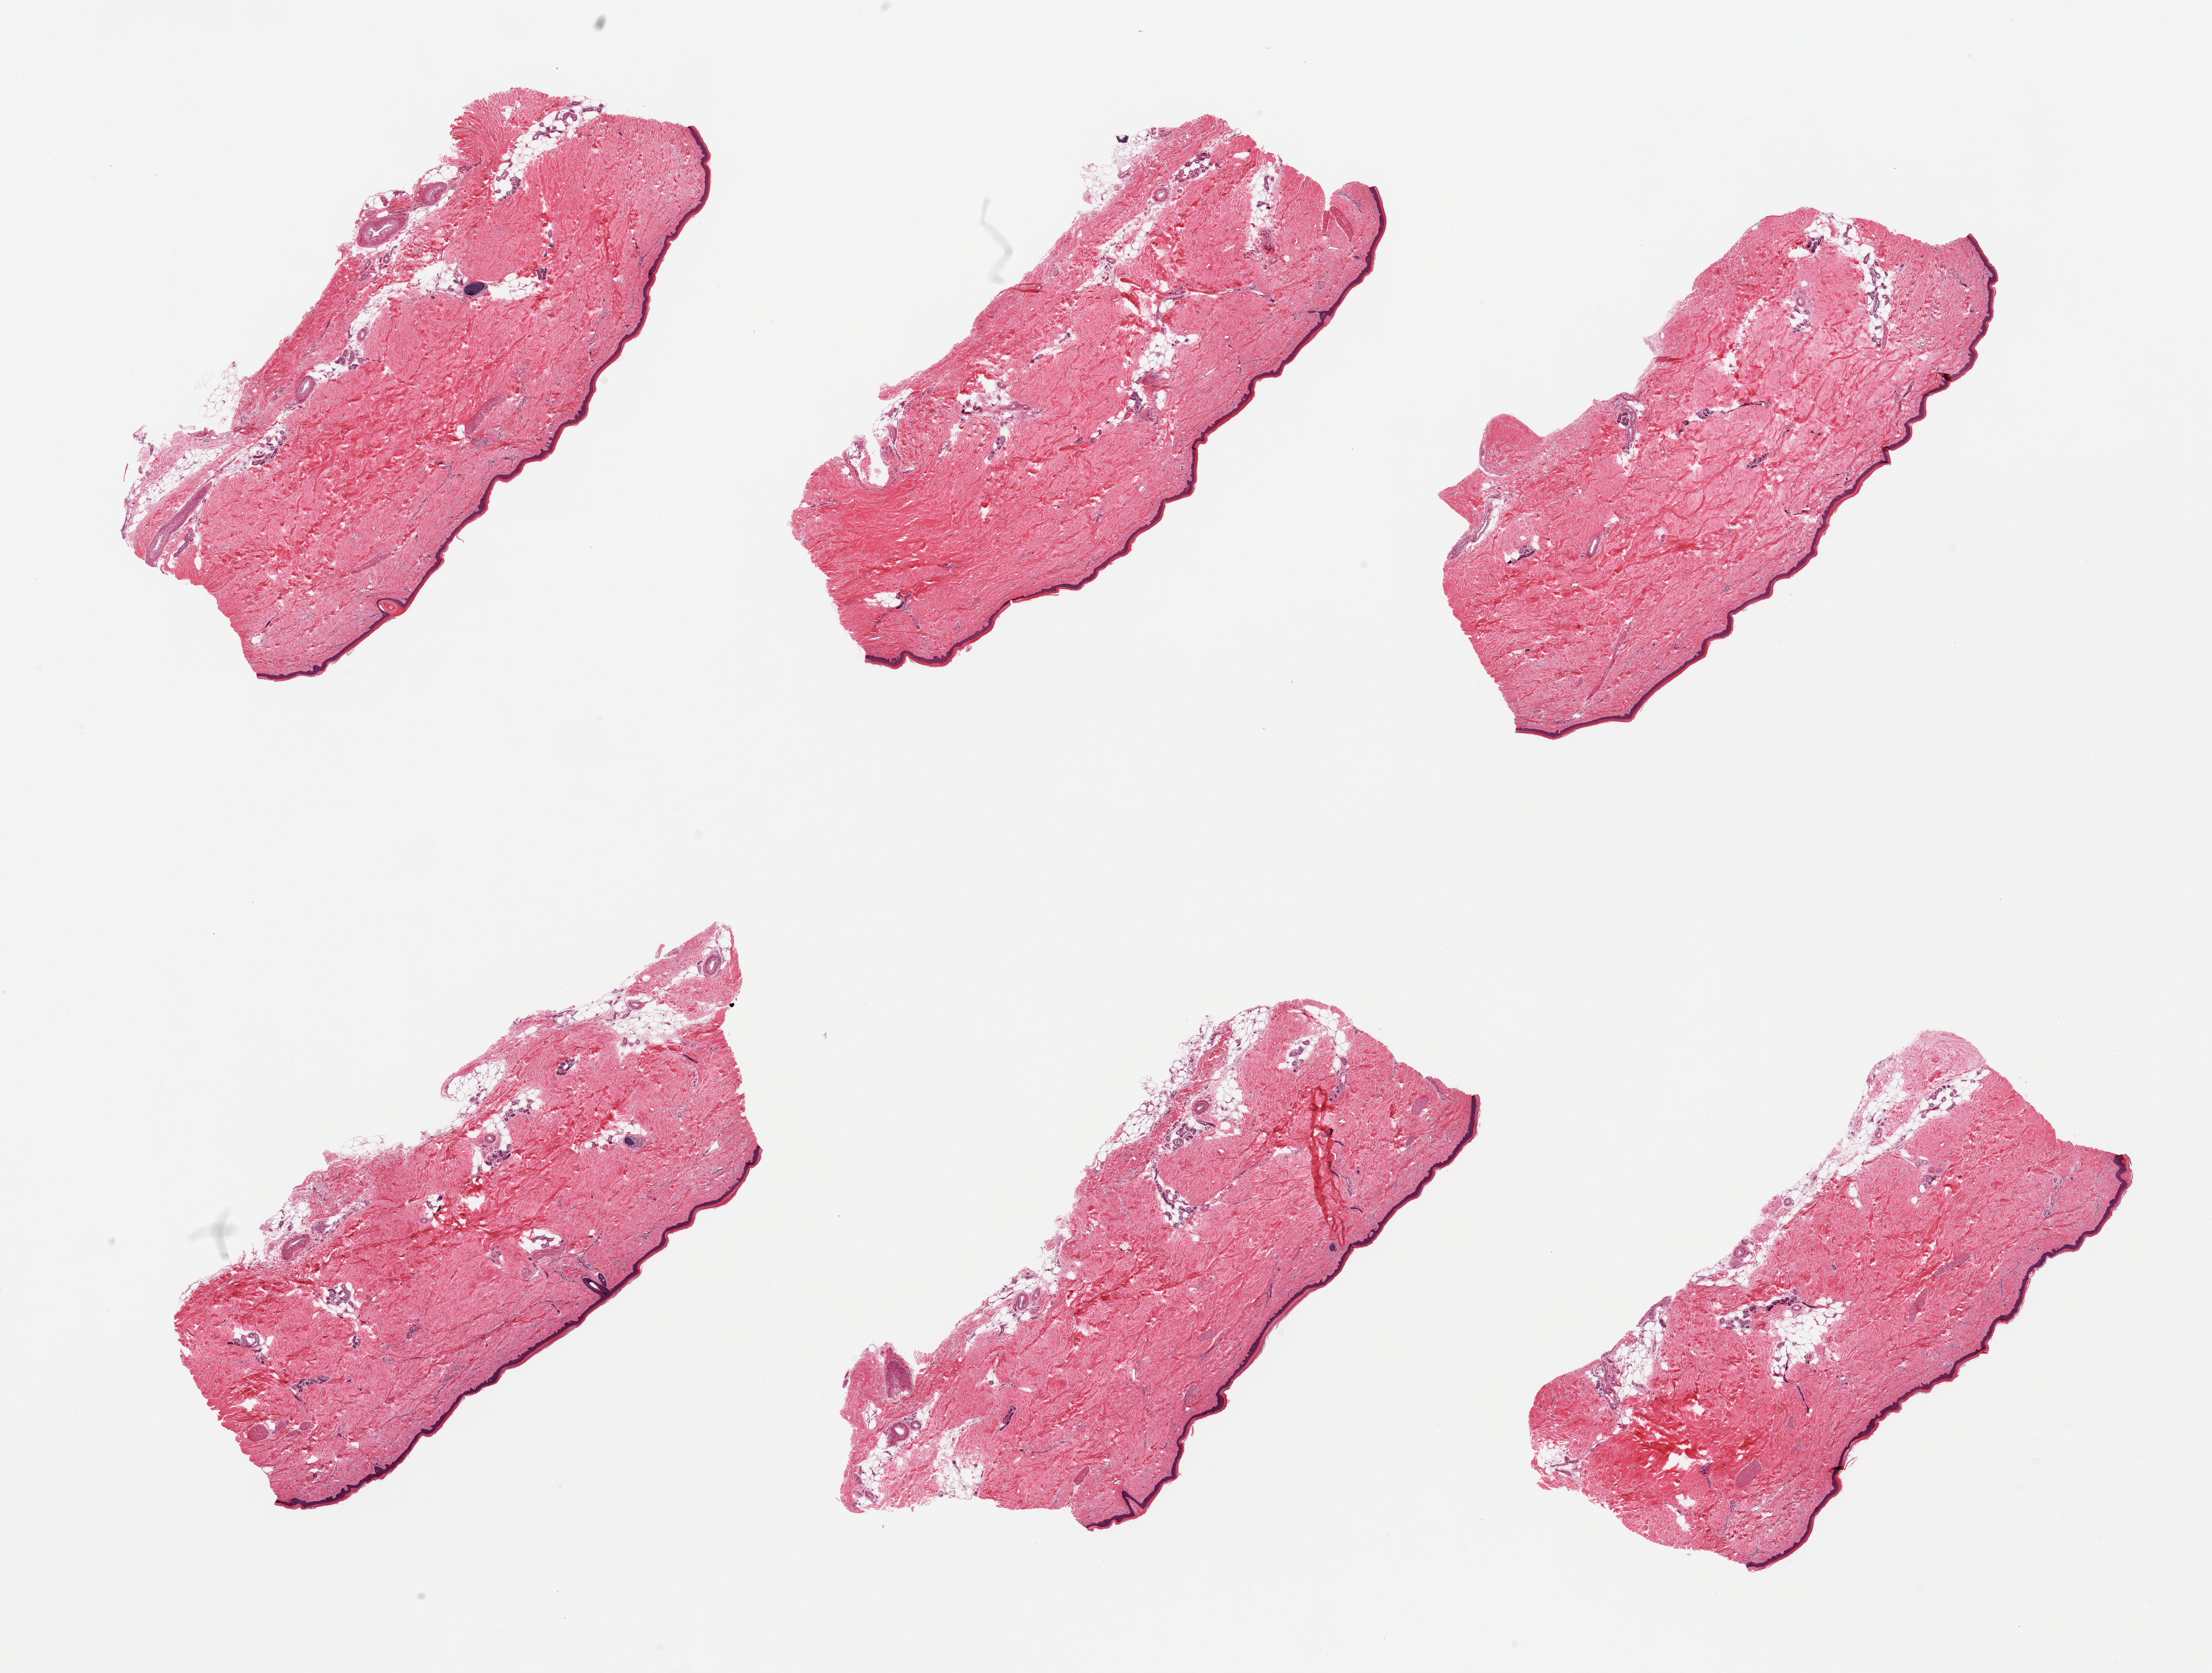
Whole-slide image, haematoxylin and eosin stain, whole scanned area (about 26.6 x 20.1 mm) shown as a low-resolution overview, PAXgene-fixed, paraffin-embedded tissue, section of skin of lower leg (target tissue), tissue donor sample. Female donor.
Reviewer comment on this tissue sample: 6 pieces; well trimmed; 10% dermal fat.